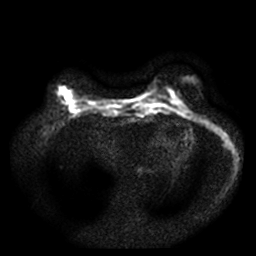
Breast MRI, one axial slice. Position 14 of 49 along the scan axis. Diffusion-weighted series; image 2 of 4 stored at this slice position (different b-values; order by instance number). 3 T. 5 mm slice thickness. 256 × 256 image matrix, field of view 340 × 340 mm. Female patient.
Outlined on this slice (outlined manually by an expert reader):
- tumour on diffusion-weighted imaging: bounding box [x1, y1, x2, y2] px = [64, 89, 71, 100]